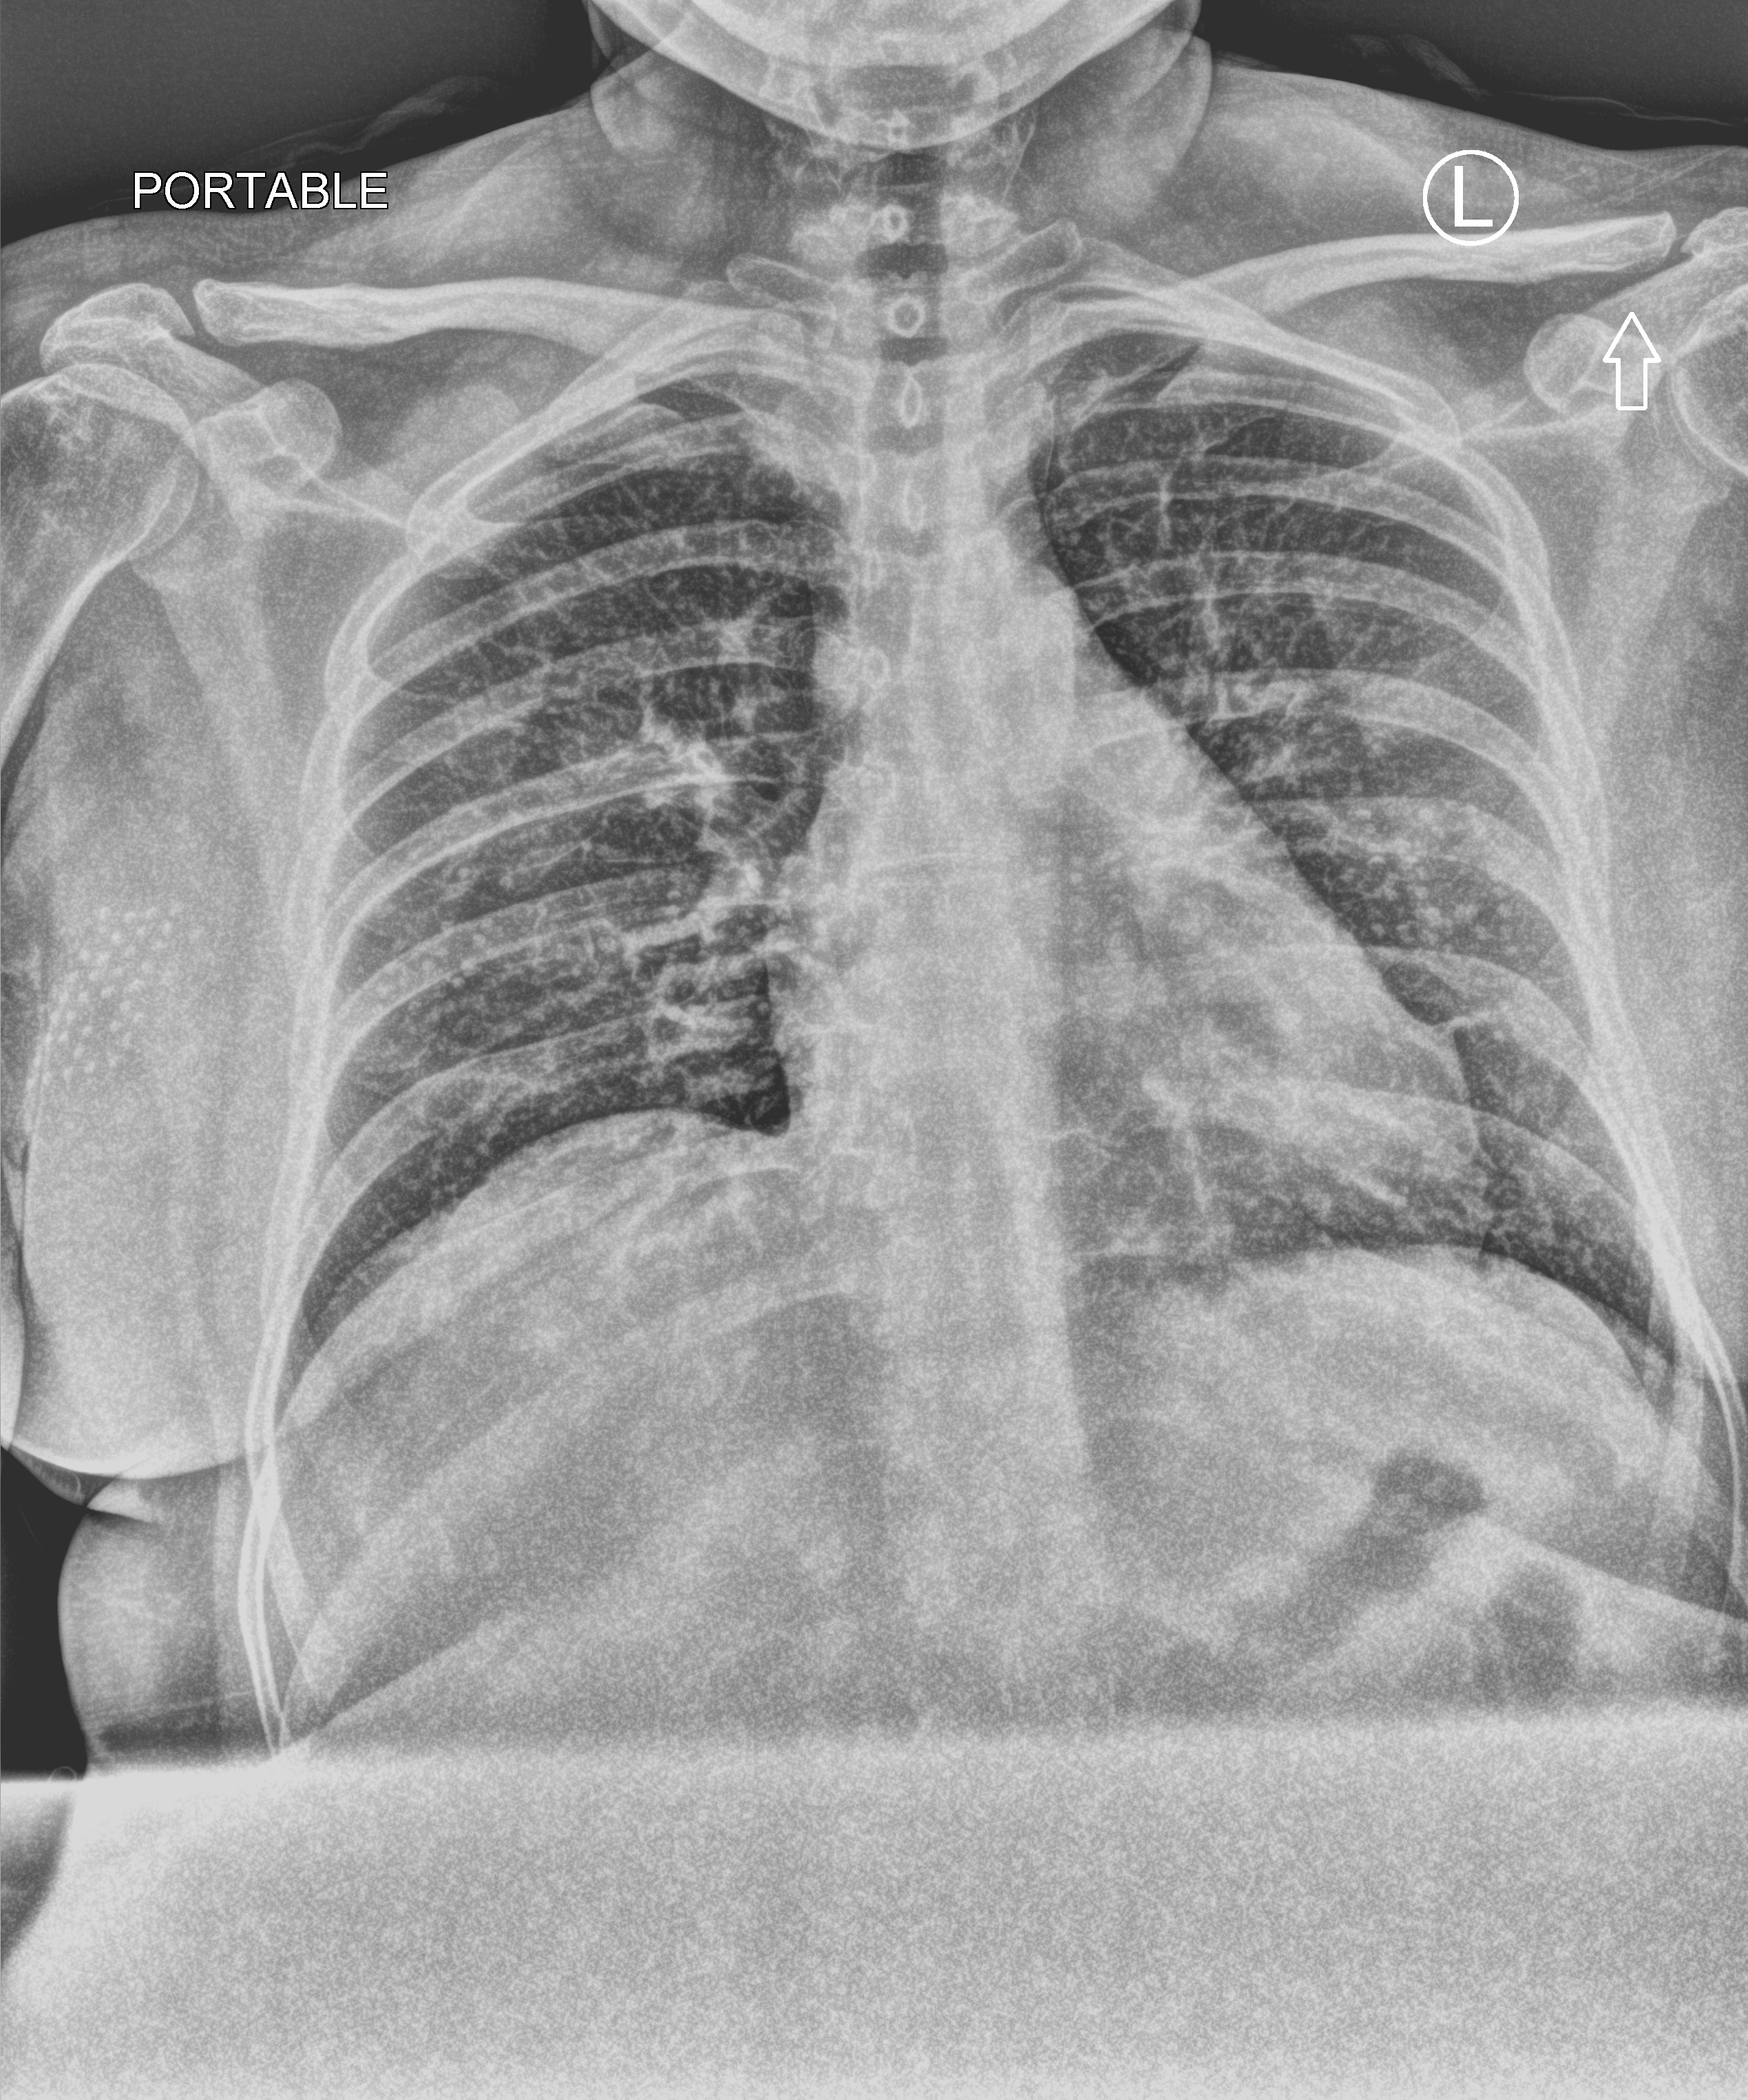
Bedside chest radiograph (computed radiography), anteroposterior (AP) projection. Patient hospitalised with COVID-19; female, aged 18–59 years.
From the hospital-stay record, not from the radiograph (when in the stay this image was taken is not recorded):
- other chronic lung disease (admission record): no
- COPD (admission record): no